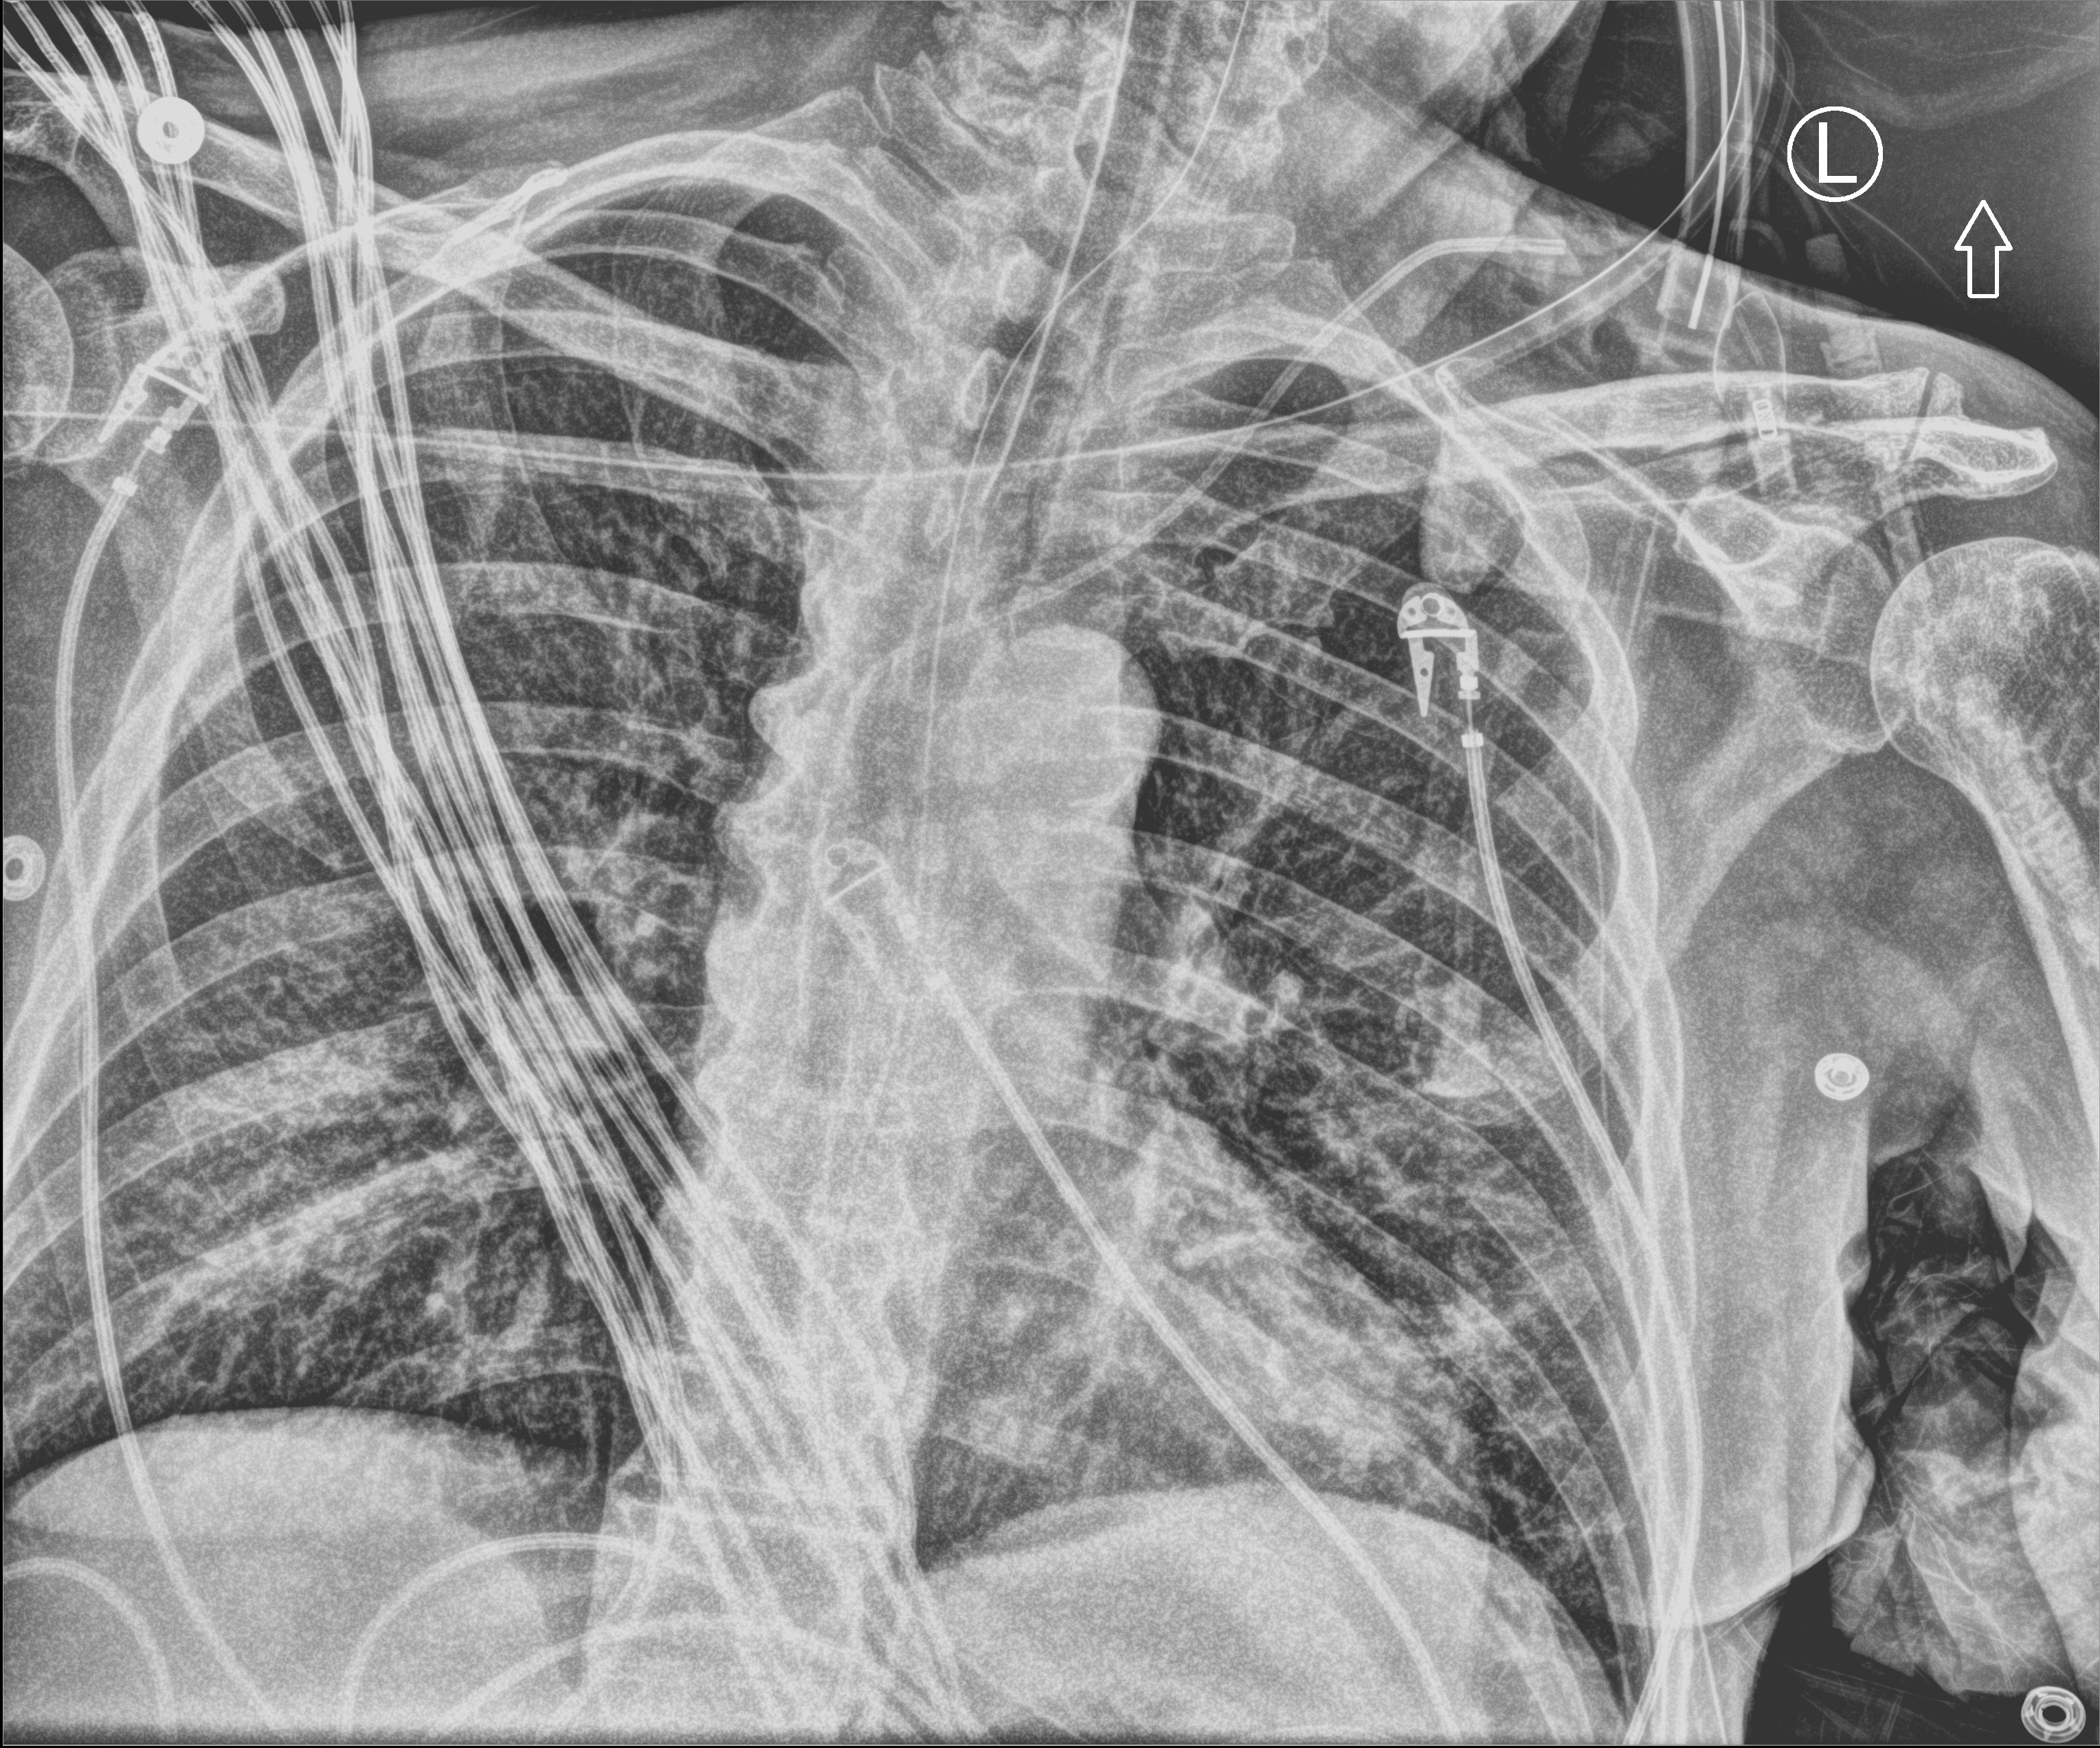
Portable chest radiograph; anteroposterior (AP) projection. Patient hospitalised with COVID-19; male, aged 60–74 years.
Admission-level facts for this patient (not findings on this image; timing relative to this image not recorded): length of hospital stay: 22 days; mechanically ventilated during this hospital stay: yes.